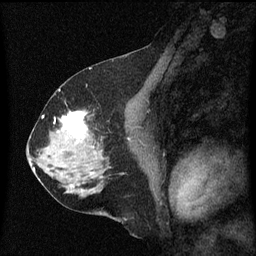
Breast MRI (dynamic contrast-enhanced), one sagittal slice; slice 32 of 60 in the series (ordered by position); dynamic contrast-enhanced series, image 2 of 3 at this slice position (ordered by acquisition); 1.5 T; TE 4.2 ms, TR 8 ms; 2 mm slice thickness; 256 × 256 image matrix, field of view 200 × 200 mm. Patient: female, 58 years.
Annotated regions visible in this slice (semi-automatic segmentation, software-assisted and operator-edited):
- analysis volume of interest (the breast-tissue region the enhancement analysis was run in; not a lesion): box from (x=56, y=112) to (x=99, y=149) px
- tumour enhancement mask (voxels above the 70 % enhancement threshold inside the analysis volume of interest): (x=61, y=112)–(x=87, y=139)